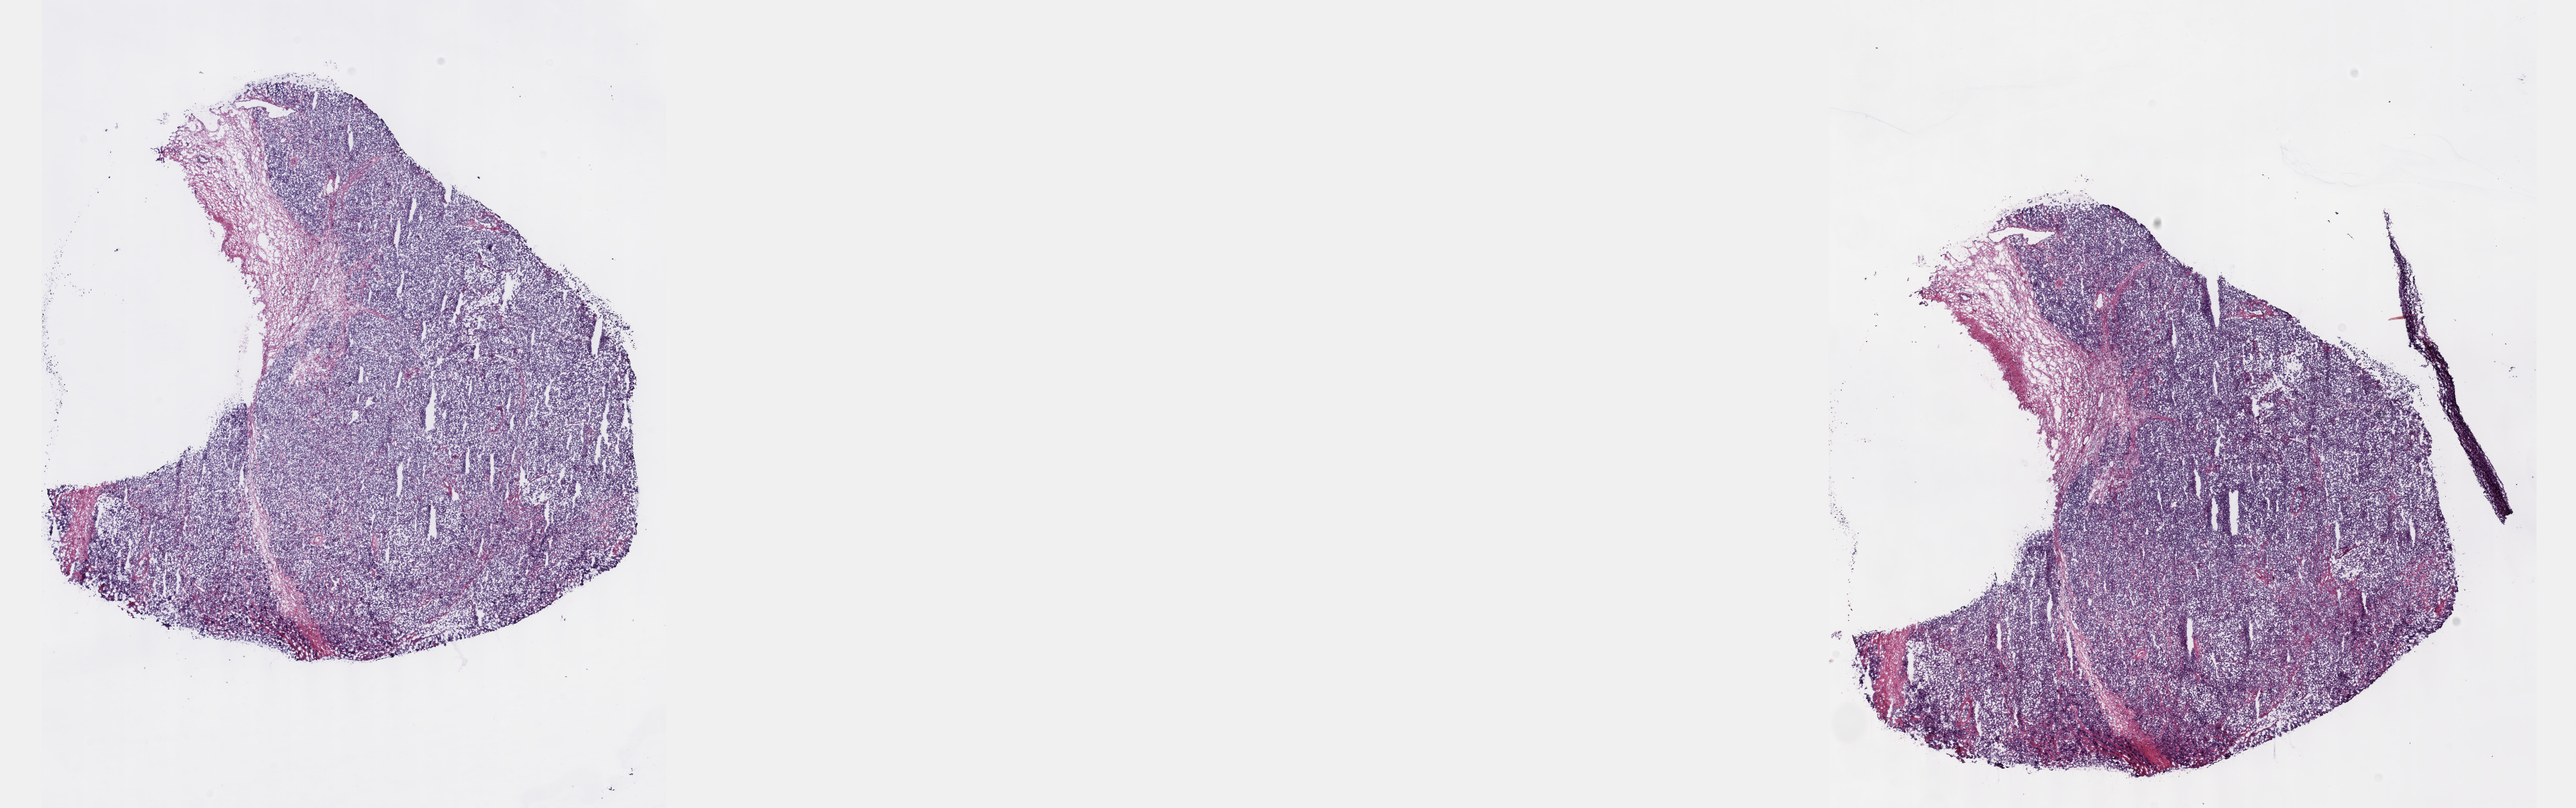
Whole-slide histology image, Hematoxylin and eosin (H&E) stained — a low-resolution overview of the entire scanned area, about 31.2 x 9.8 mm, frozen section from the top of the tissue portion, testis, primary tumour sample. Male patient; age at initial diagnosis 21 years. Pathologist review of this section (percent, as recorded): tumour cells 70%, tumour nuclei 70%, normal cells 0%, stromal cells 20%, necrosis 10%. Inflammatory infiltration, as recorded: lymphocyte infiltration 40%, monocyte infiltration 20%, neutrophil infiltration 20%.
AJCC pathologic stage: IB (6th edition). Histologic diagnosis: Seminoma, NOS.